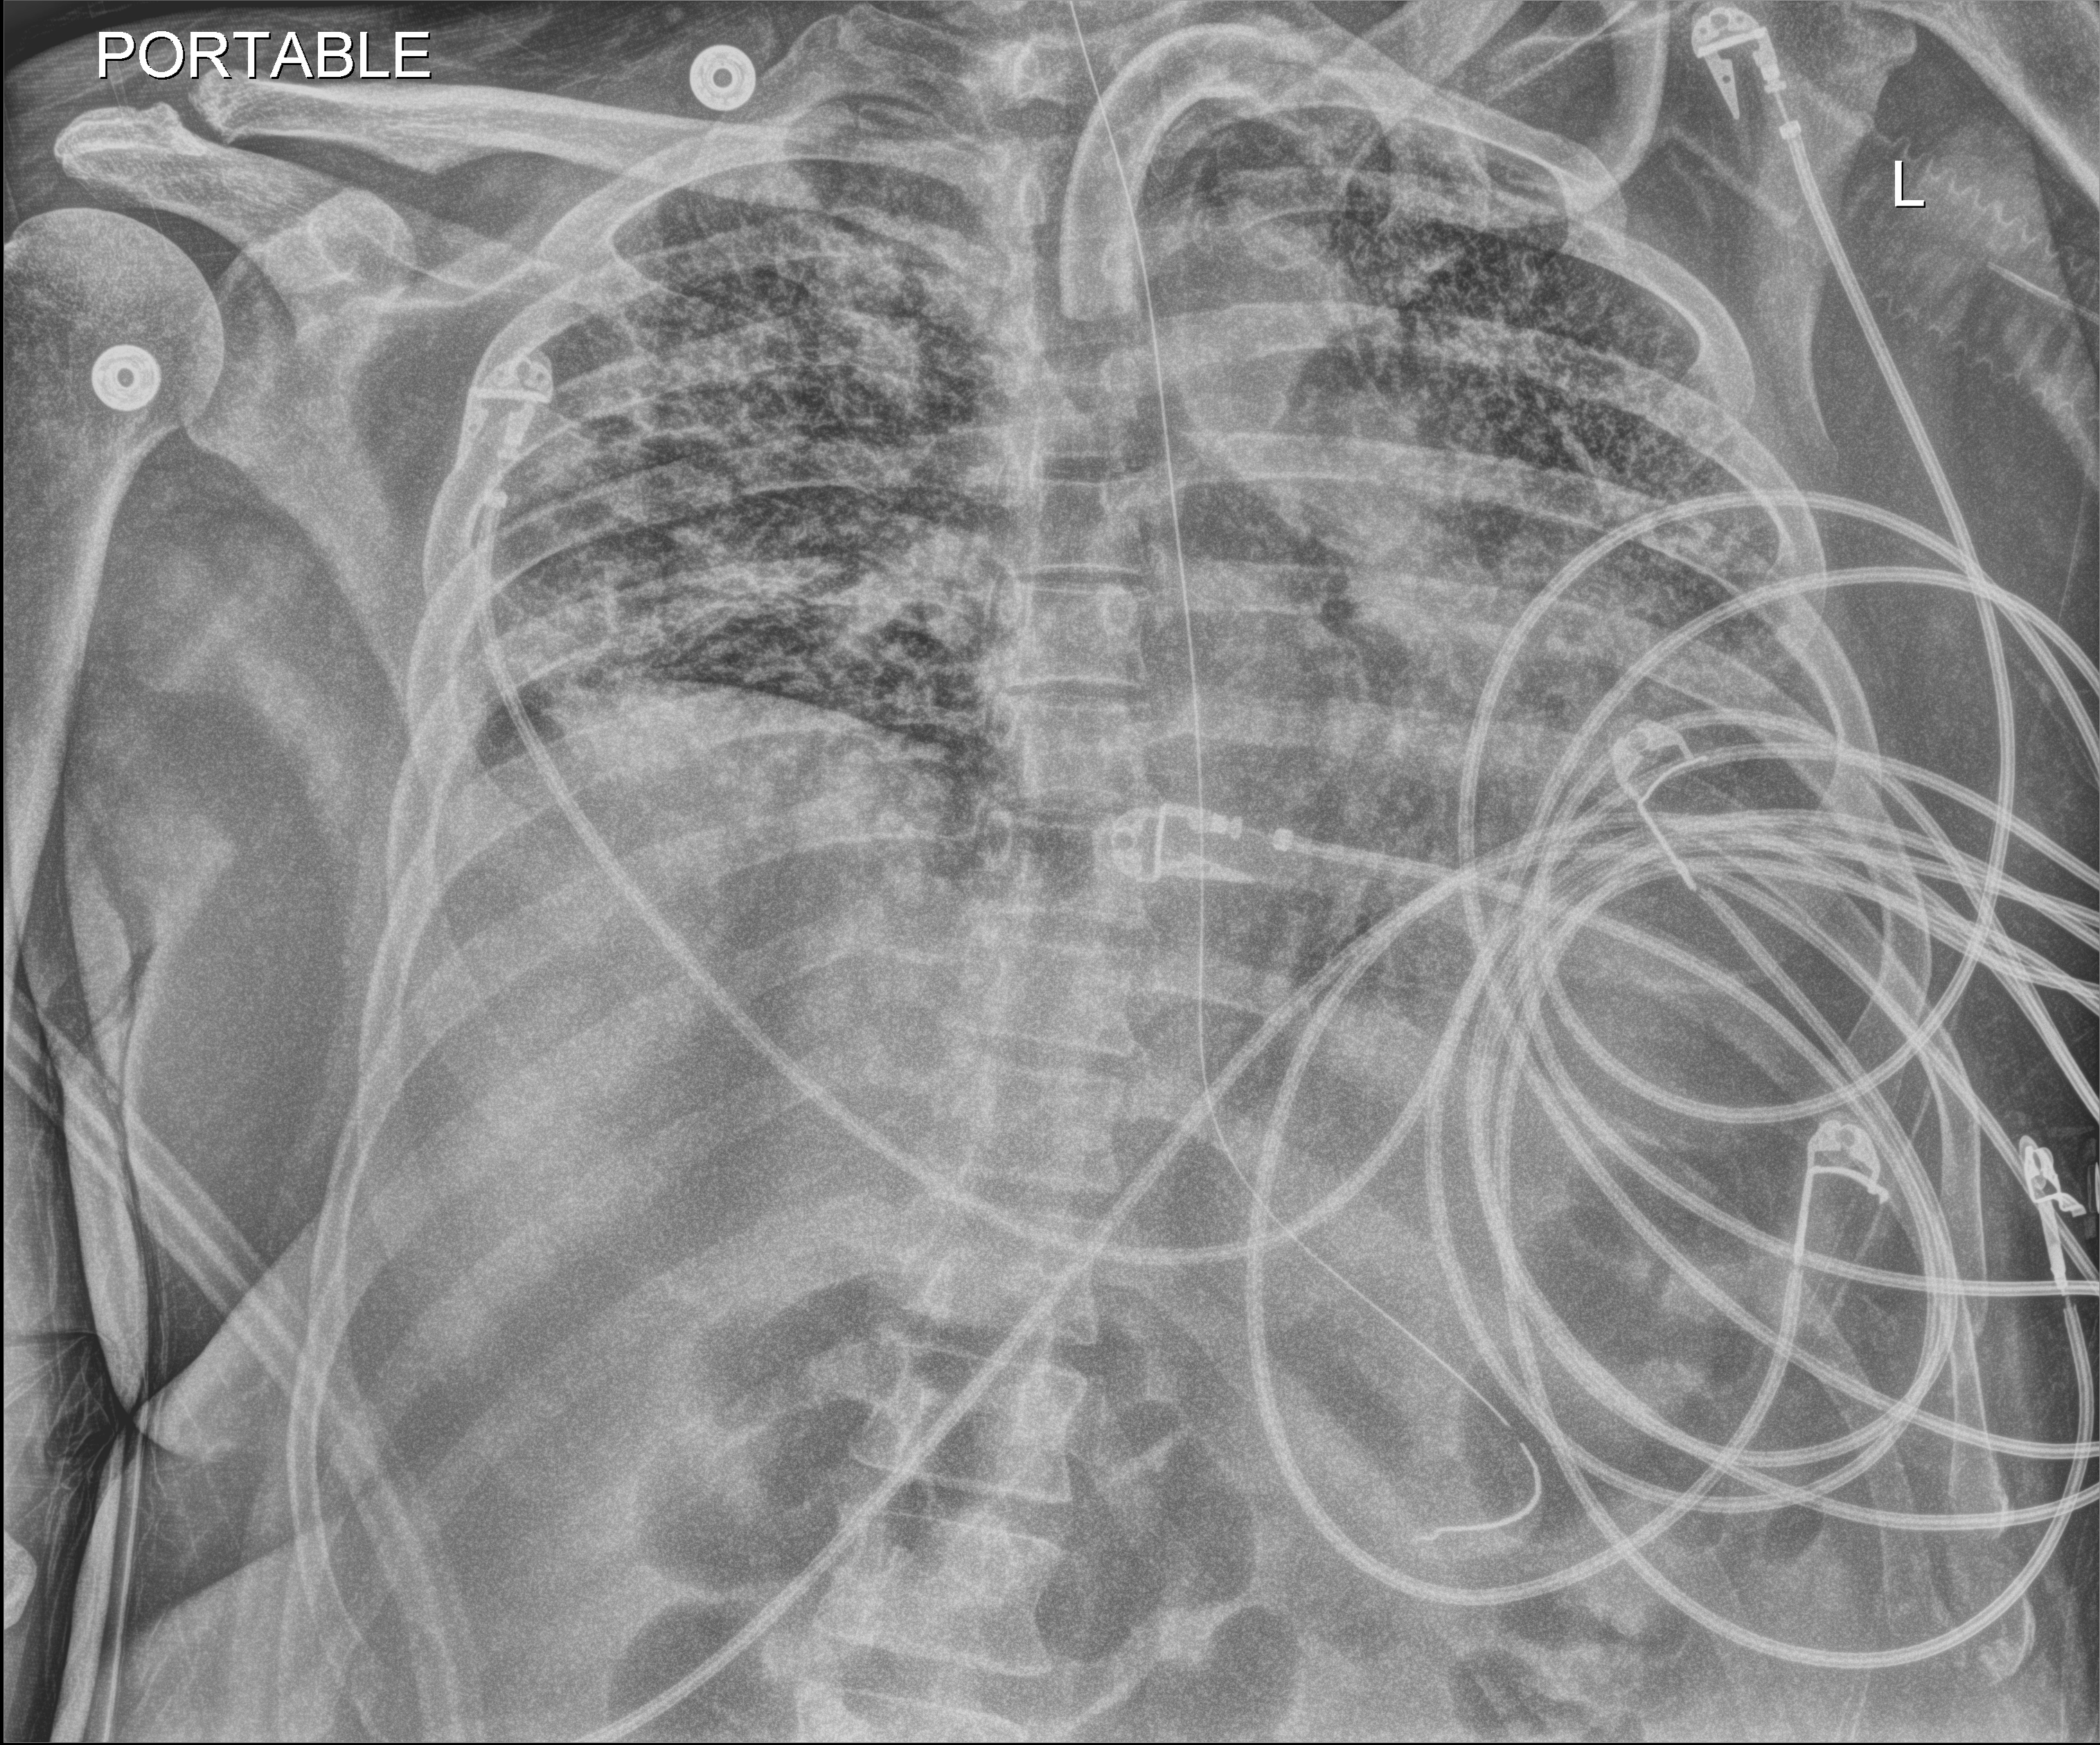
Portable chest radiograph, anteroposterior (AP) projection. Patient hospitalised with COVID-19; male, aged 18–59 years.
Admission-level facts for this patient (not findings on this image; timing relative to this image not recorded):
- diabetes (admission record): no
- admitted to intensive care during this hospital stay: yes
- mechanically ventilated during this hospital stay: yes